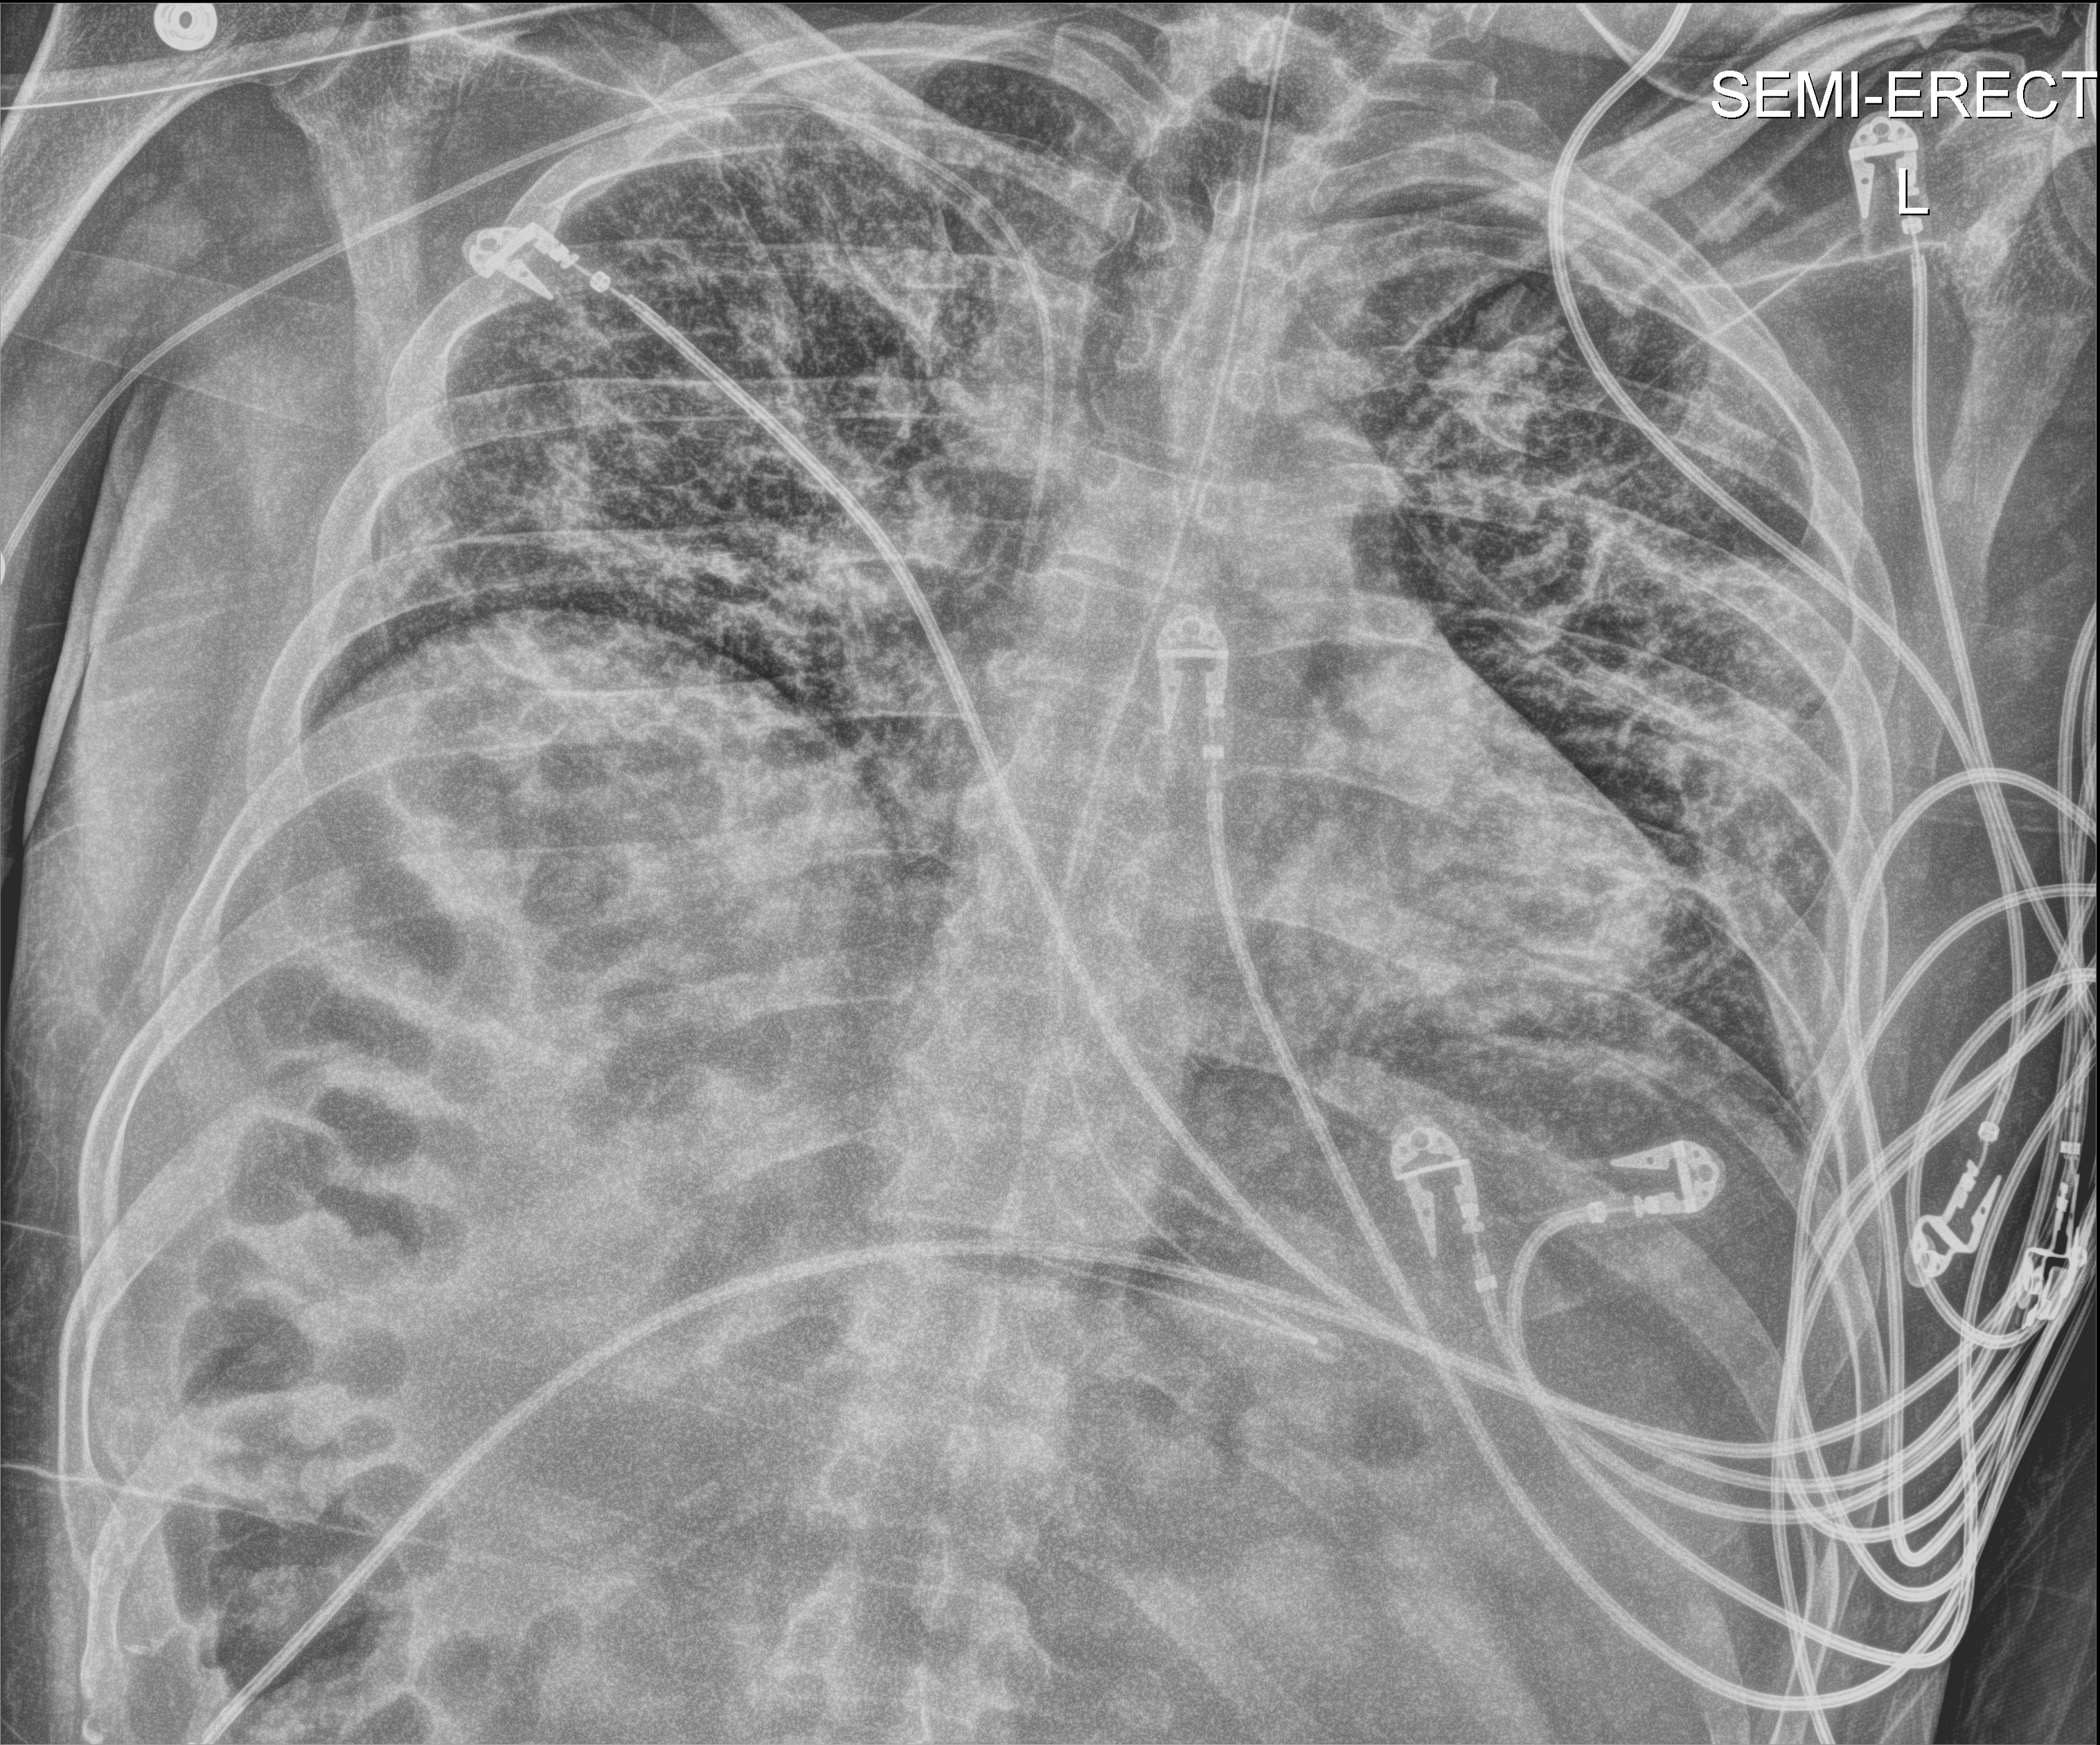
Bedside chest radiograph (digital radiography), anteroposterior (AP) projection. Male patient hospitalised with COVID-19, age 18–59 years.
Hospital-stay facts (about this admission, not read from this image; timing relative to this image not recorded): mechanically ventilated during this hospital stay: yes; admitted to intensive care during this hospital stay: yes.